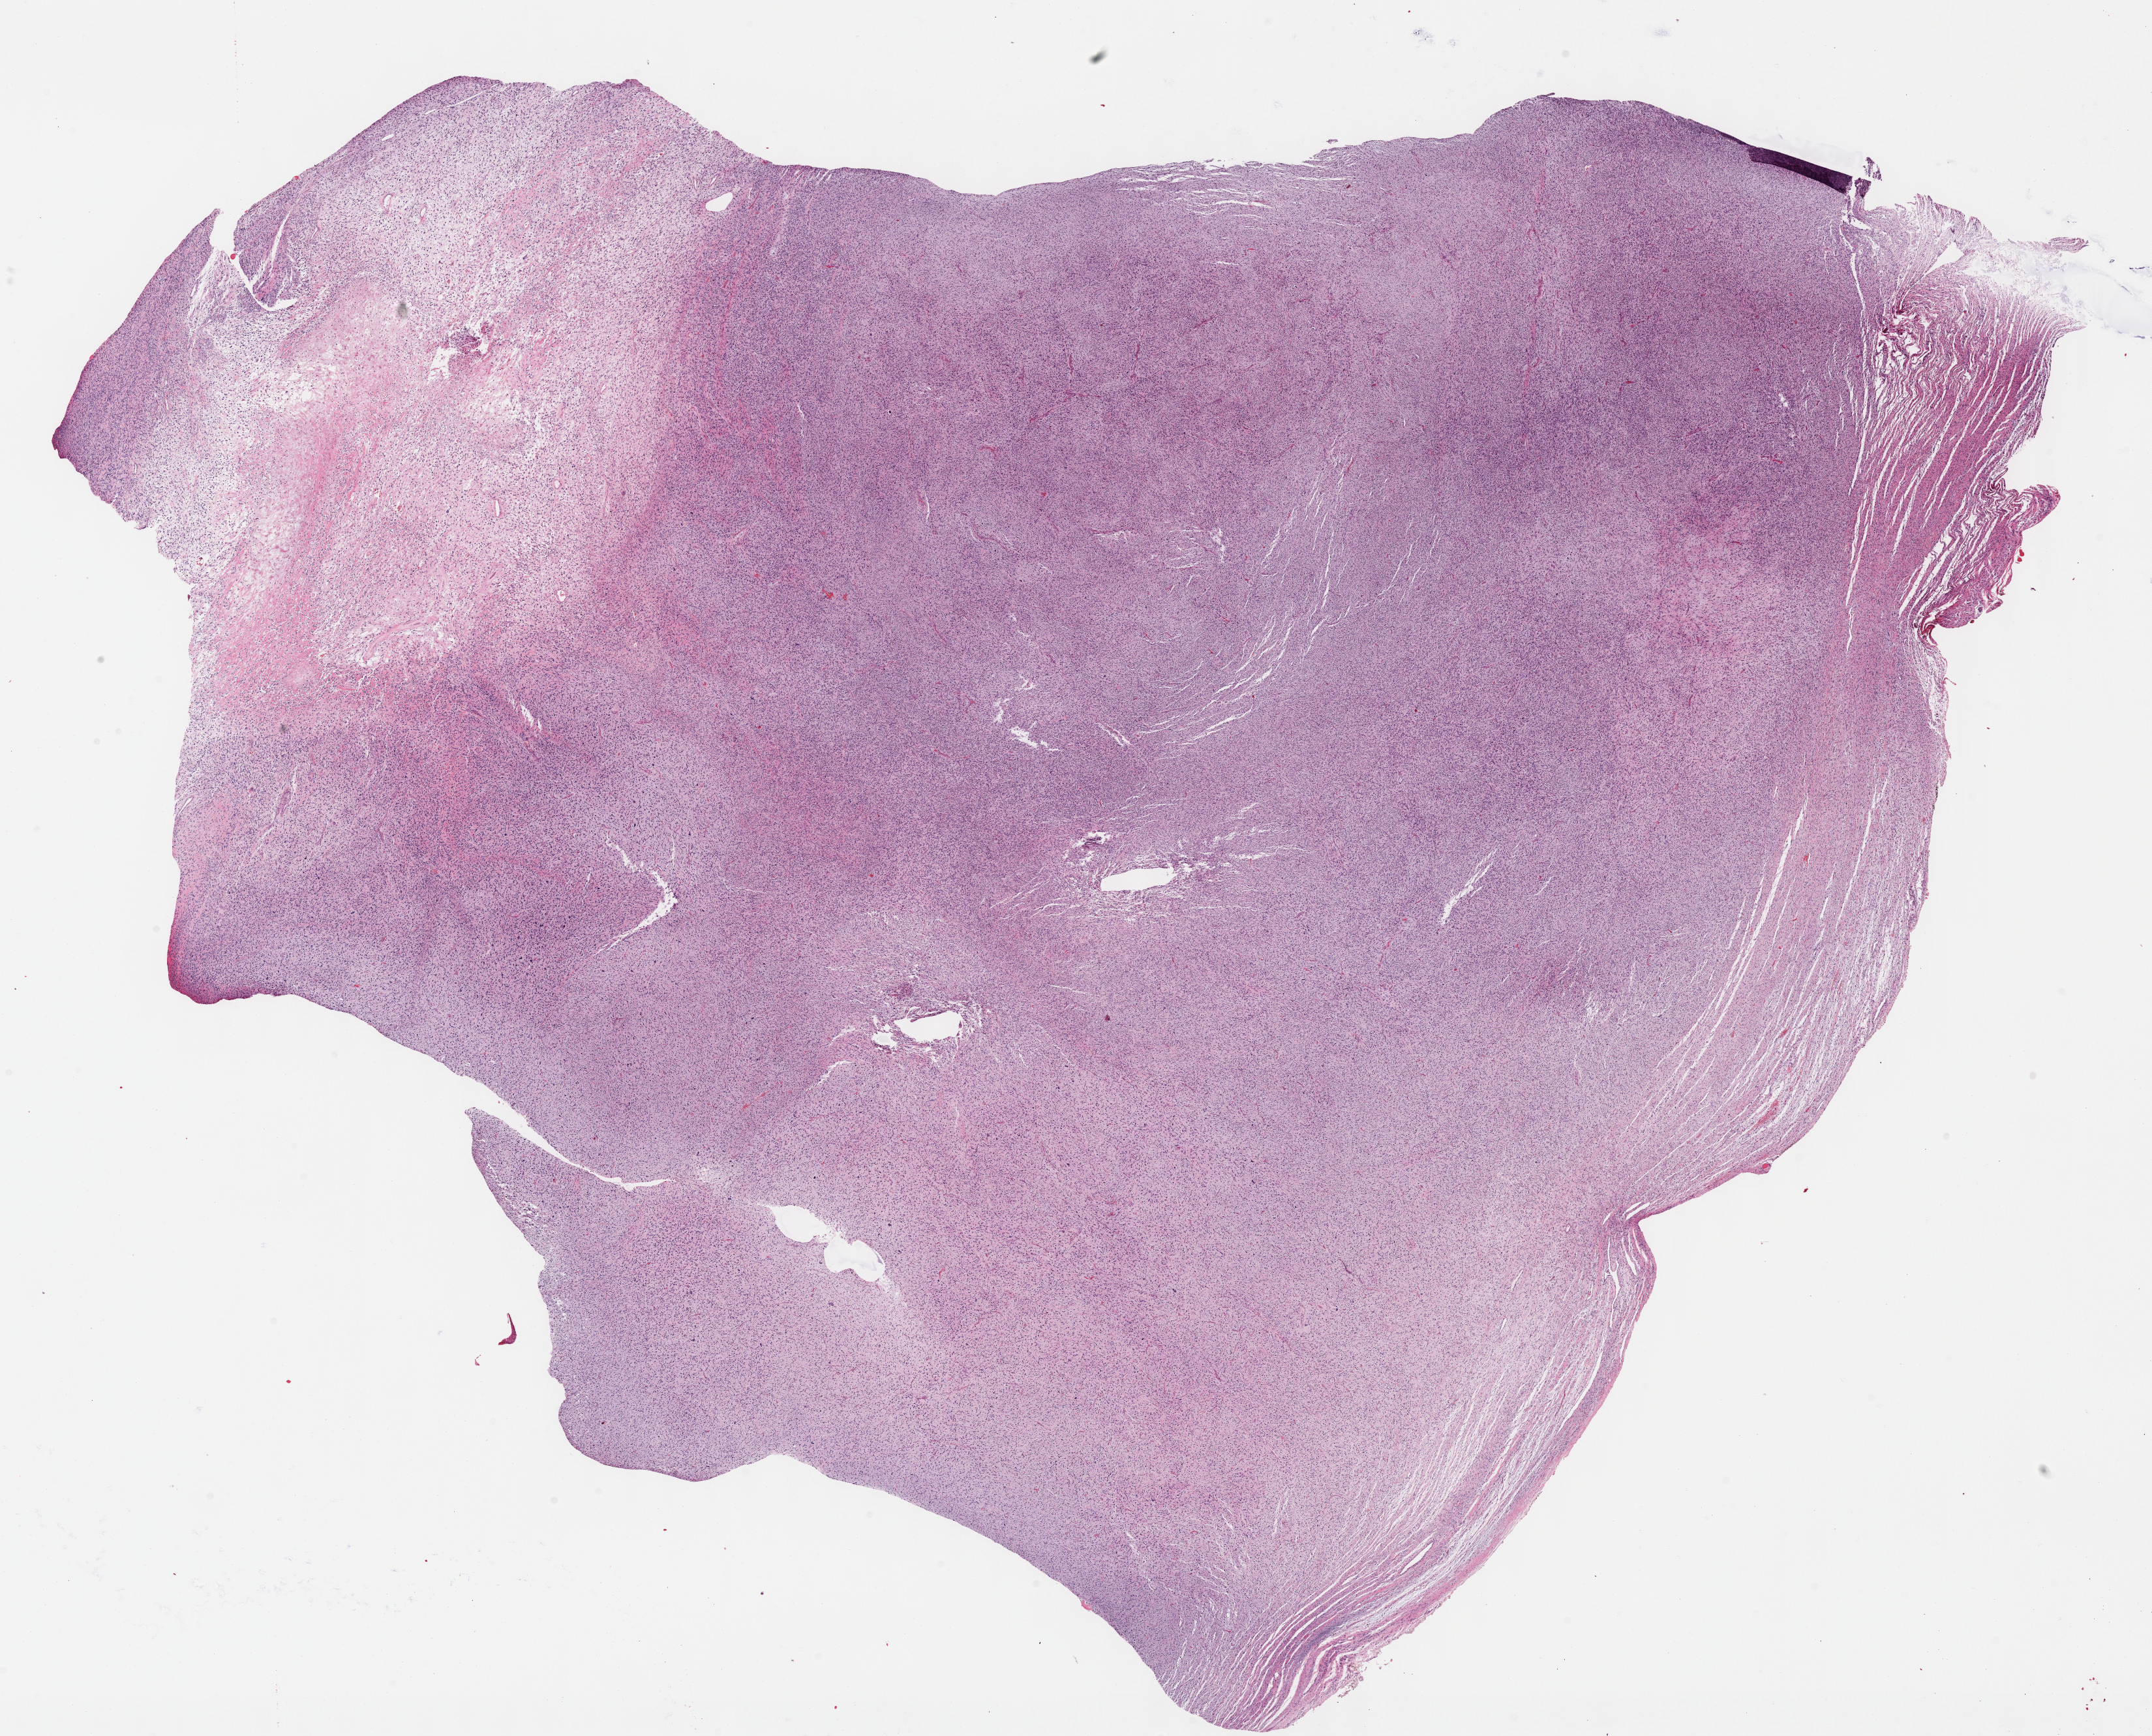
Hematoxylin and eosin (H&E) stained whole-slide image — low-resolution overview of the scanned area, about 26.7 x 21.5 mm (slide scanned at 40x), formalin-fixed paraffin-embedded (FFPE) diagnostic section, primary tumour sample from the retroperitoneum and peritoneum. Male patient; age at initial diagnosis 72 years.
Pathologic diagnosis: Sarcoma, NOS.